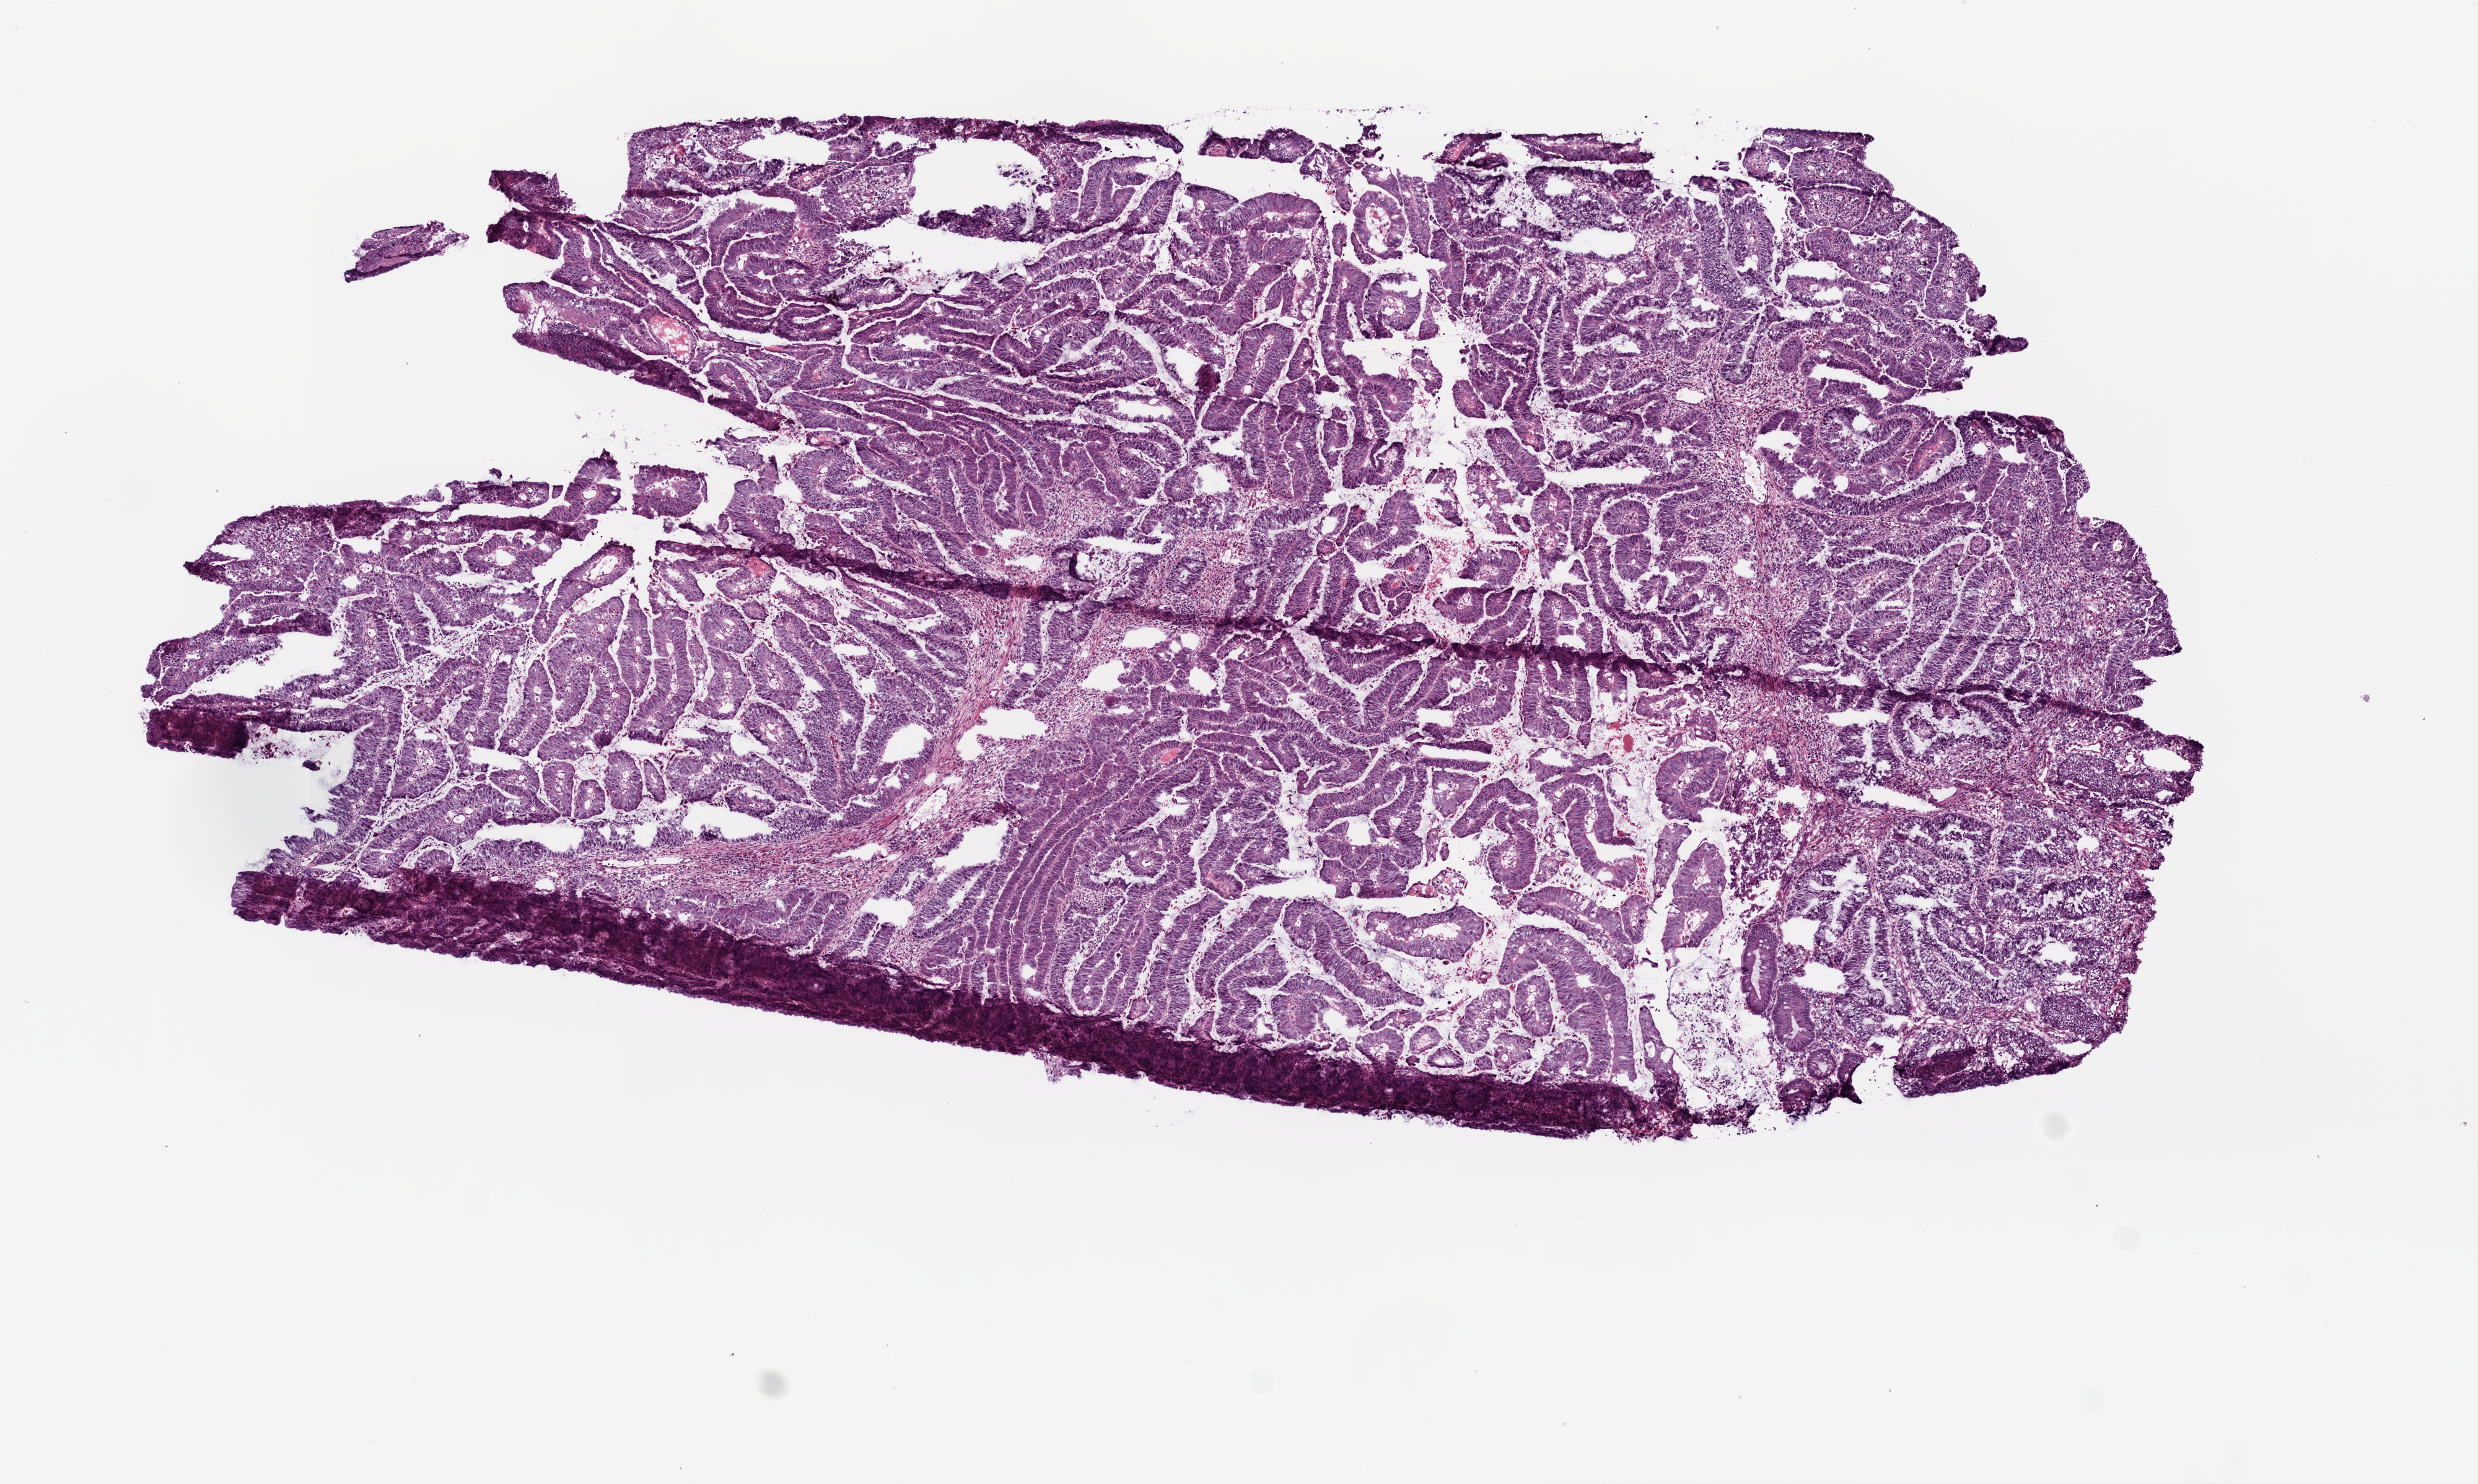
Digitized H&E-stained tissue section (whole slide), a low-resolution overview of the entire scanned area, about 8.0 x 4.8 mm, frozen section, primary tumour sample from the colon. Male patient; age at initial diagnosis 78 years. Composition of this section per pathologist review: tumour cells 80%, tumour nuclei 90%.
Histologic diagnosis: Mucinous adenocarcinoma (sigmoid colon).